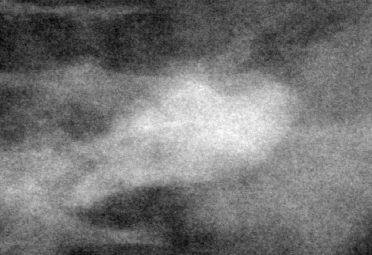
Crop from a digitized film mammogram around one marked abnormality; left breast; MLO view; BI-RADS breast density category 4 (scale 1–4).
Finding: mass, shape irregular, margins circumscribed / obscured; BI-RADS assessment category 4; pathology (as recorded): benign.